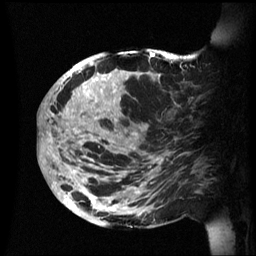
Breast MRI (dynamic contrast-enhanced), one sagittal slice; slice 26 of 60 in the series (ordered by position); dynamic contrast-enhanced series, image 2 of 3 at this slice position (ordered by acquisition); 1.5 T; TE 4.2 ms, TR 8.4 ms; 2.4 mm slice thickness; 256 × 256 image matrix, field of view 230 × 230 mm. Female patient, age 48 years.
Annotated regions visible in this slice (semi-automatically segmented with operator editing):
- analysis volume of interest (the breast-tissue region the enhancement analysis was run in; not a lesion): box from (x=42, y=49) to (x=202, y=228) px
- tumour enhancement mask (voxels above the 70 % enhancement threshold inside the analysis volume of interest): (x=42, y=52)–(x=163, y=225)